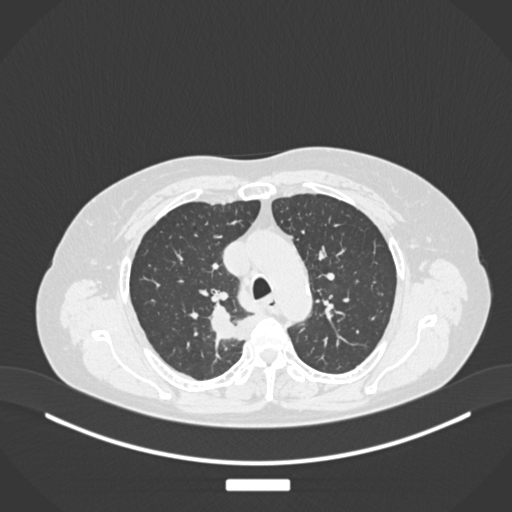
Chest CT, one axial slice; slice 186 of 237 in the series (ordered by position); lung window (W 1500 / L -600 HU); 1 mm slice thickness; 512 × 512 image matrix, field of view 400 × 400 mm. Patient: female, 62 years. From the clinical record (not read from this slice): clinical TNM (as recorded): T1c N1 M0.
Structures marked on this image (rectangle marked by the reading radiologist):
- lung tumour (recorded histology: squamous cell carcinoma): bounding box [x1, y1, x2, y2] px = [210, 305, 249, 349]